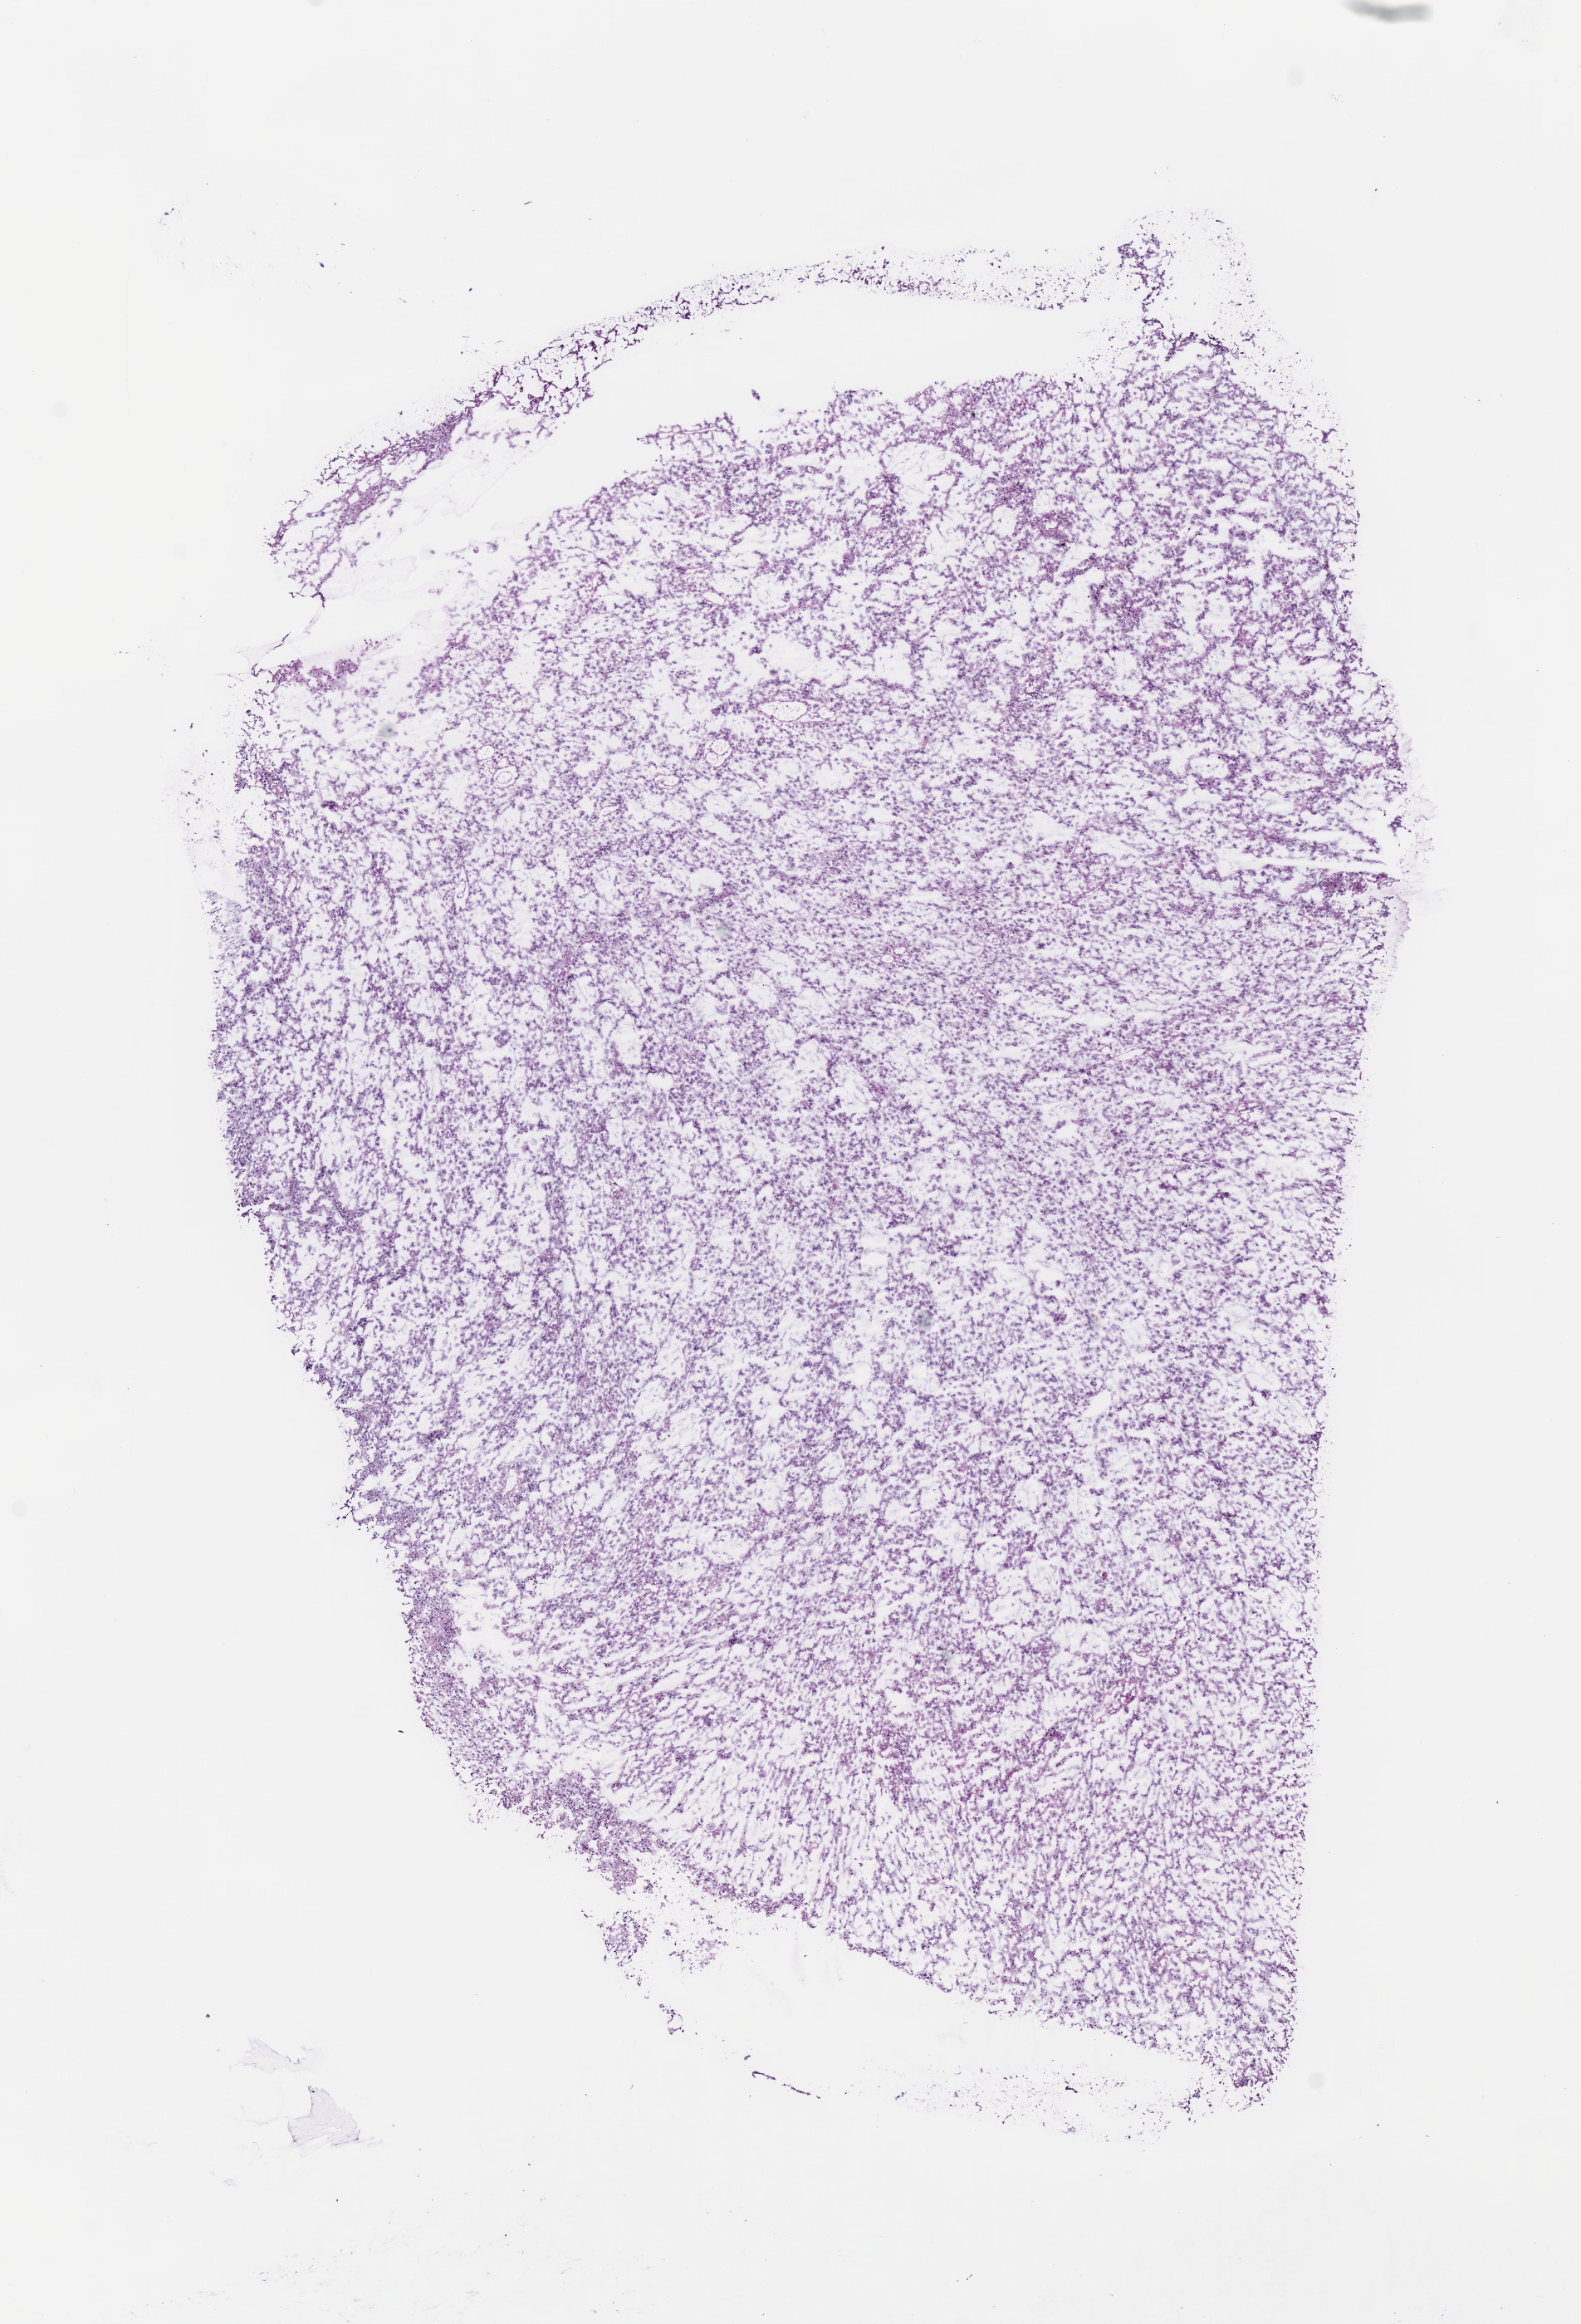
Whole-slide histology image, H&E, low-resolution overview of the scanned area, about 7.5 x 11.0 mm (from a 40x scan); frozen section from the top of the tissue portion; sample: primary tumour, brain. Male patient; age at initial diagnosis 50 years. Histologic grade: G2 (moderately differentiated). Pathologist review of this section (percent, as recorded): tumour cells 100%, tumour nuclei 80%, normal cells 0%, stromal cells 0%, necrosis 0%.
* diagnosis: Astrocytoma, NOS (cerebrum)